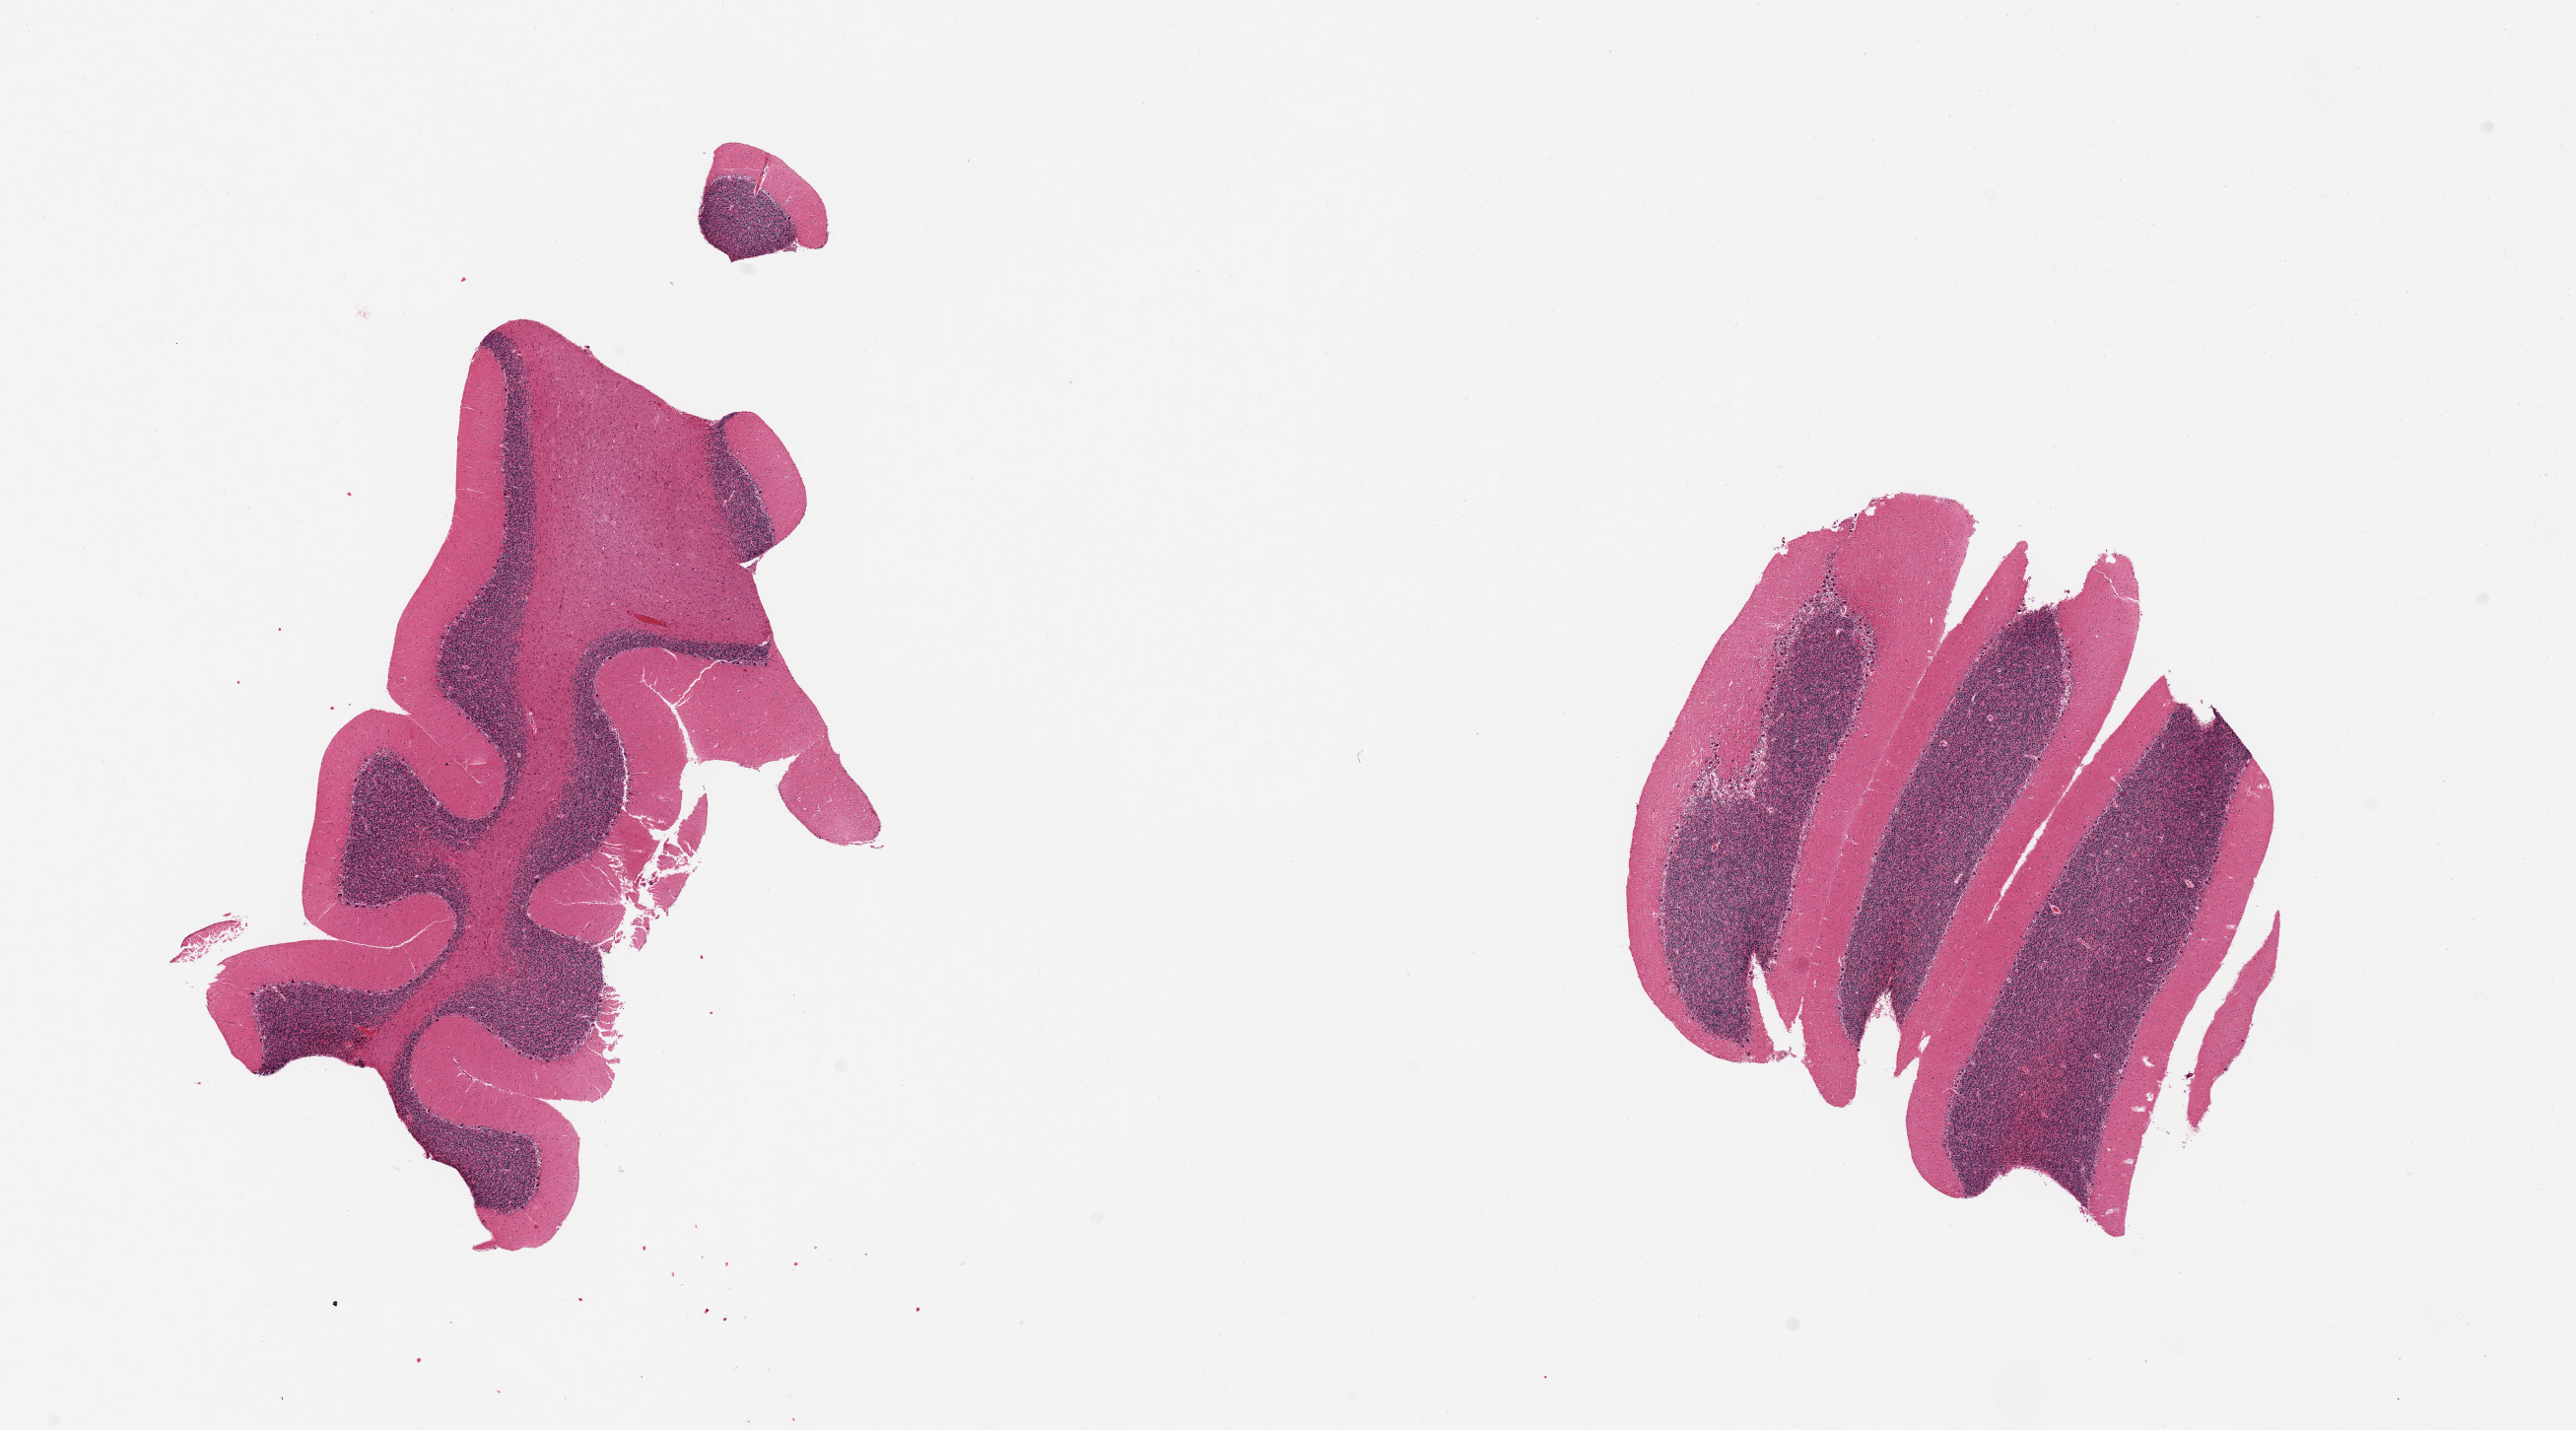
Digitized H&E-stained section — a low-resolution overview of the entire scanned area, about 20.7 x 11.5 mm; PAXgene-fixed paraffin-embedded (PFPE) section; section of cerebellum (target tissue); tissue donor sample. Donor: female.
- reviewer comment on this tissue sample: 2 pieces